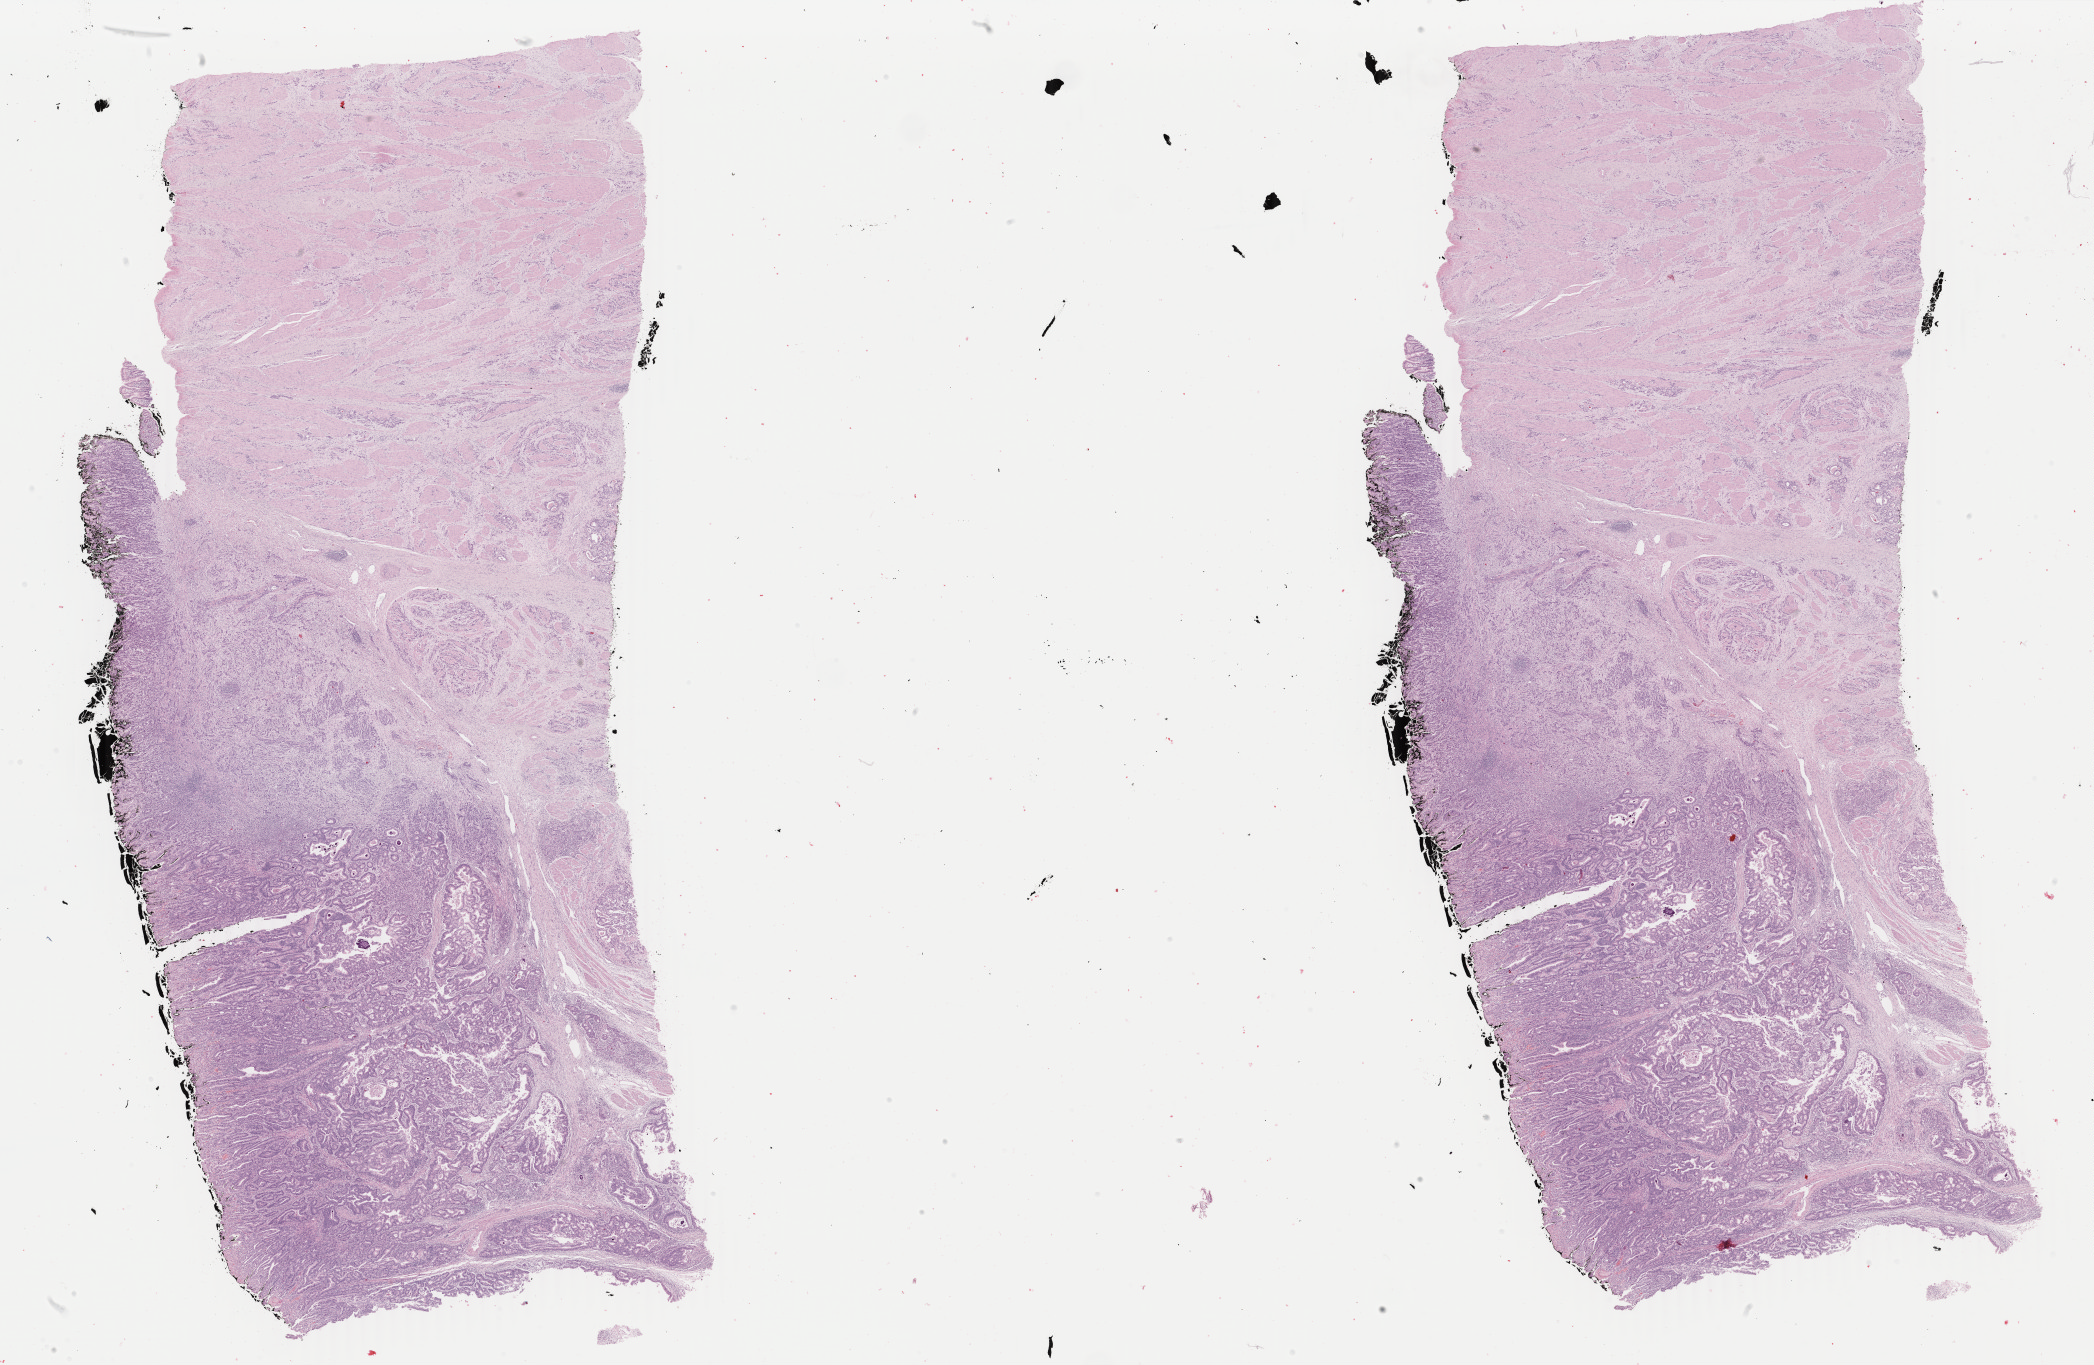
Whole-slide histology image, H&E, whole scanned area (about 33.3 x 21.7 mm, from a 40x scan) shown as a low-resolution overview; FFPE section; sample: primary tumour, stomach. Male patient; age at initial diagnosis 80 years. Histologic grade: G3 (poorly differentiated).
Diagnosis: Tubular adenocarcinoma (body of stomach). AJCC pathologic stage: IIIA (7th edition). Lymph nodes positive (case pathology): 6 of 19 examined.